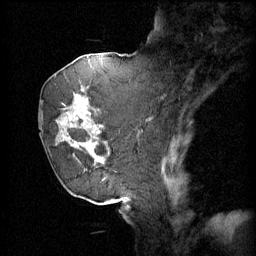
Breast MRI (dynamic contrast-enhanced), one sagittal slice. Position 20 of 60 along the scan axis. 4 images stored at this slice position (order not interpretable as contrast timing). 1.5 T. TE 4.2 ms, TR 11 ms. 256 × 256 image matrix. Patient: female, 72 years.
Structures marked on this image (semi-automatically segmented with operator editing):
- analysis volume of interest (the breast-tissue region the enhancement analysis was run in; not a lesion): bounding box [x1, y1, x2, y2] px = [46, 68, 109, 163]
- tumour enhancement mask (voxels above the 70 % enhancement threshold inside the analysis volume of interest): [63, 68, 109, 161]